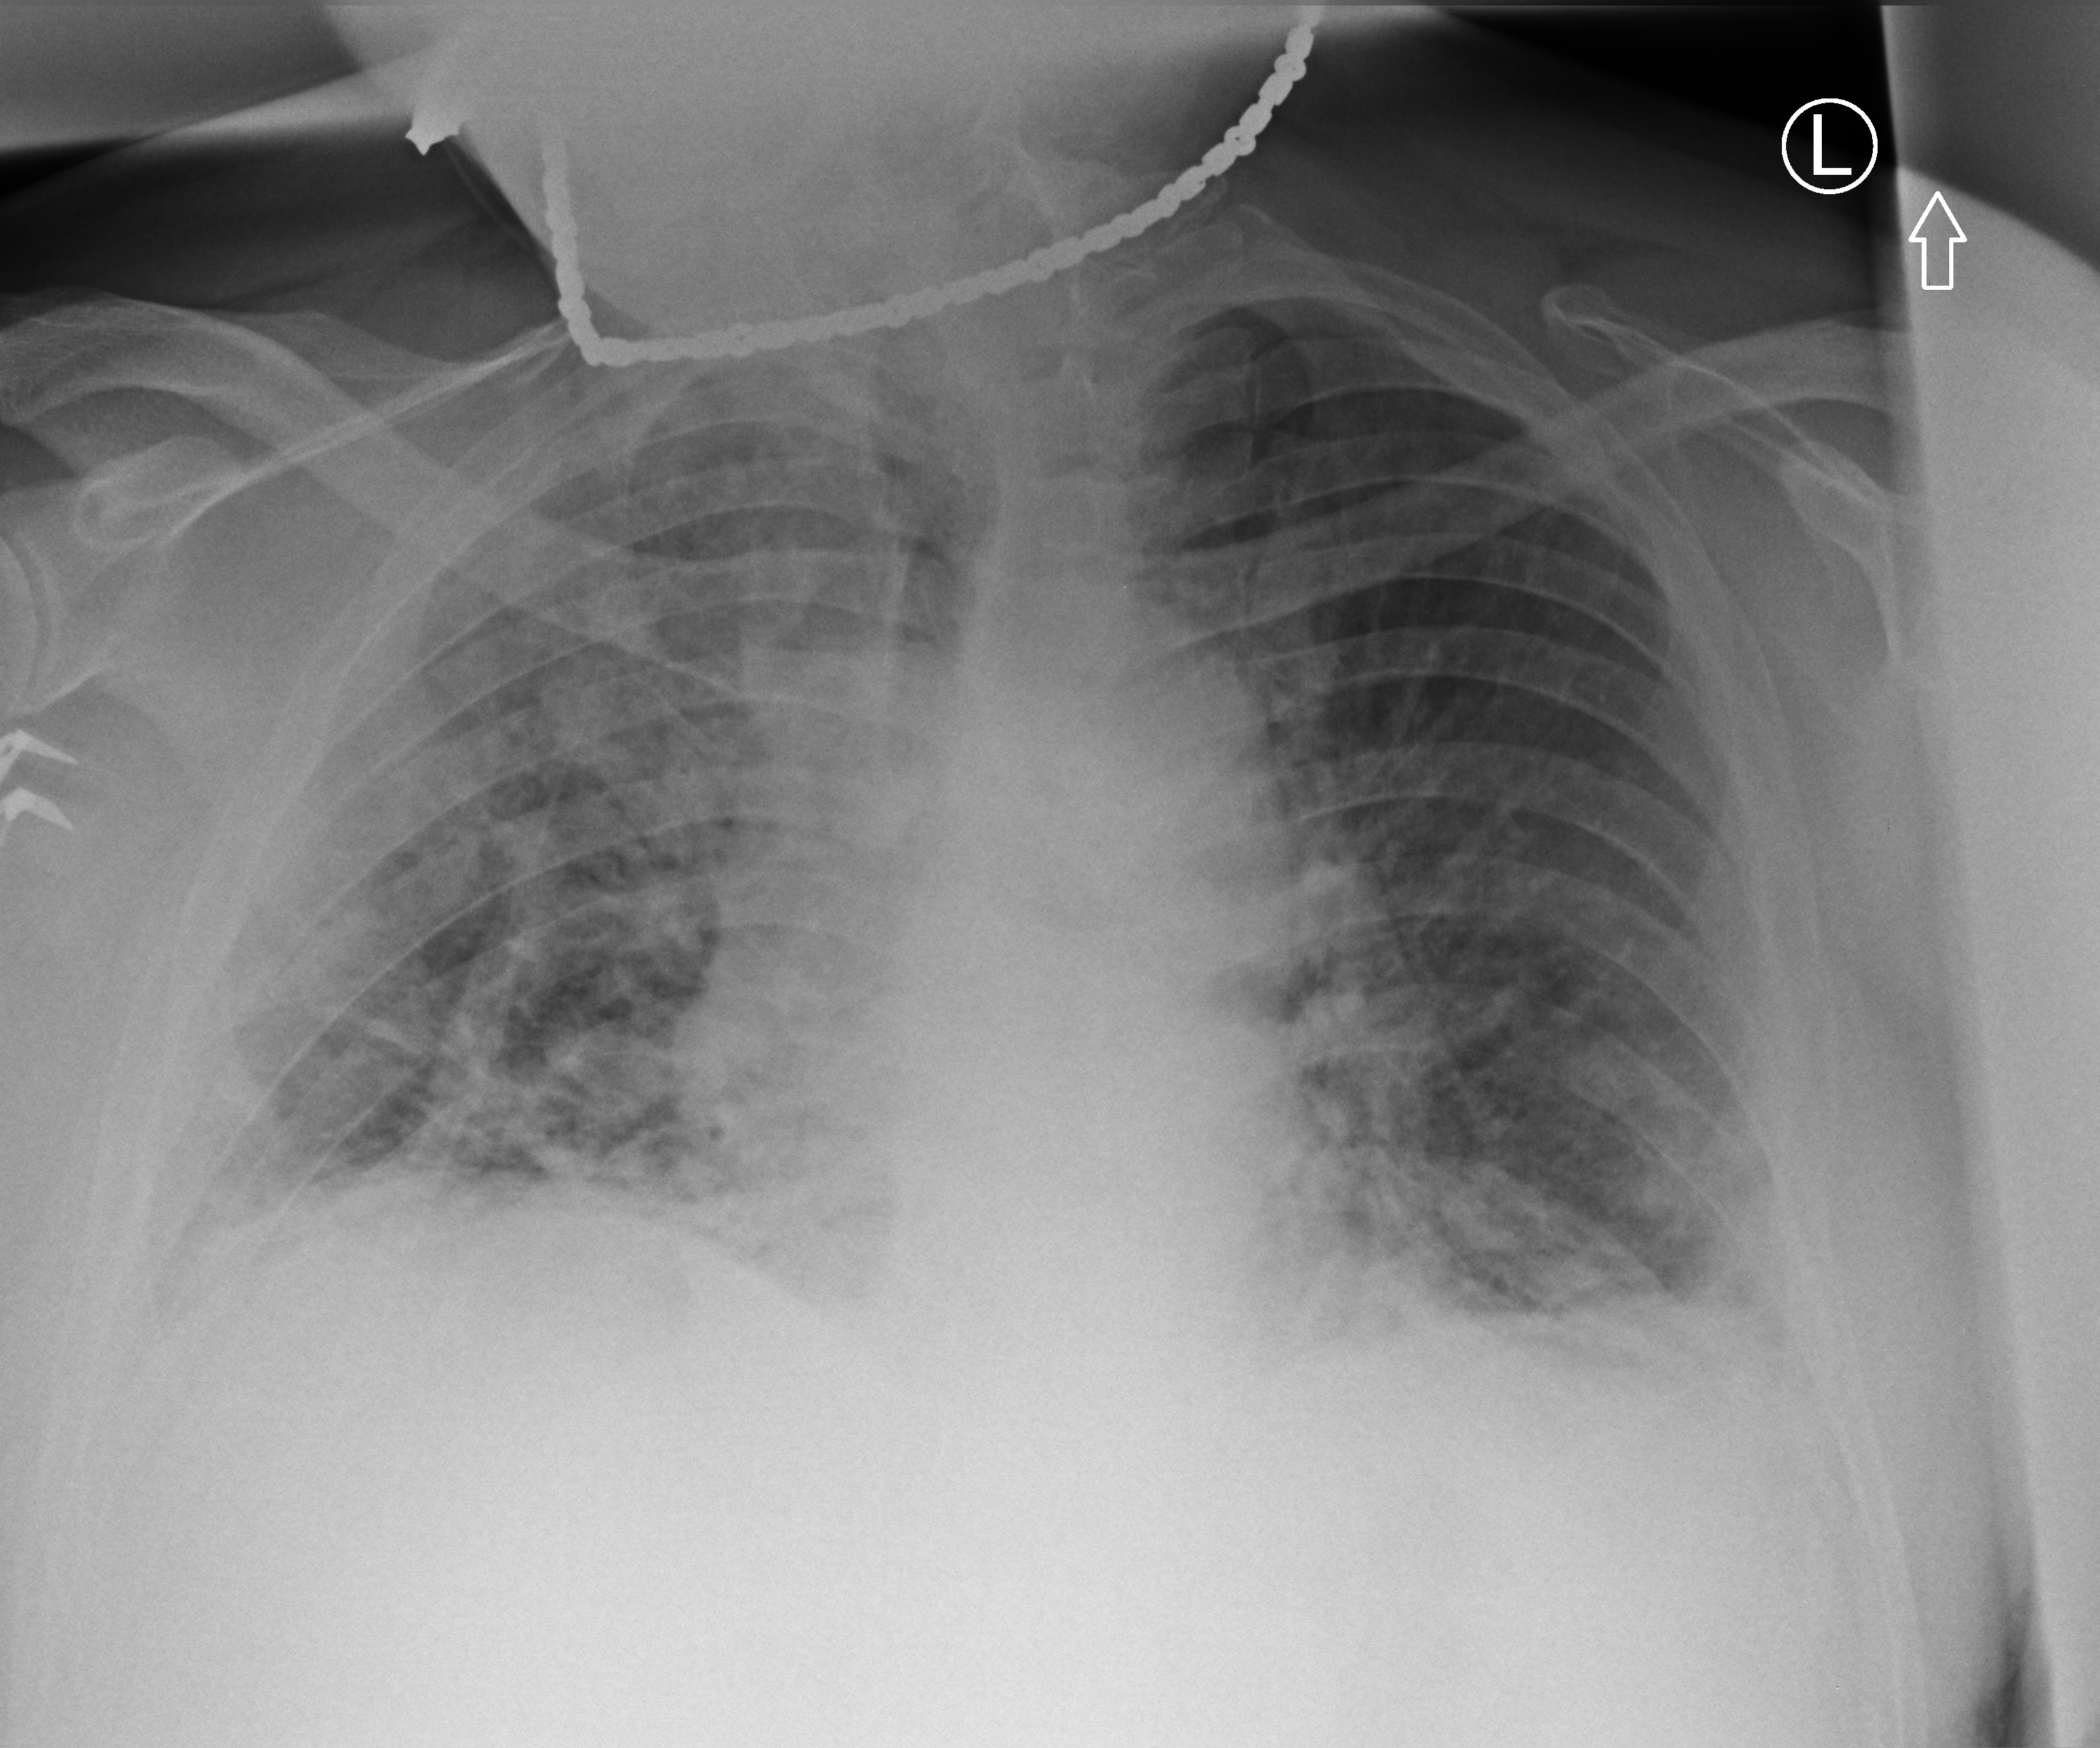
Portable chest radiograph. Male patient hospitalised with COVID-19, age 18–59 years.
From the hospital-stay record, not from the radiograph (when in the stay this image was taken is not recorded): admitted to intensive care during this hospital stay: no; smoking status (admission record): former; mechanically ventilated during this hospital stay: no.